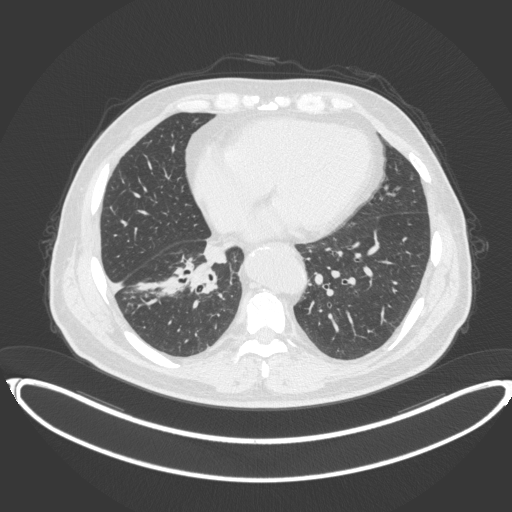
Chest CT, one axial slice. Position 151 of 383 along the scan axis. Reconstruction kernel B31f. Lung window (W 1500 / L -600 HU). 1 mm slice thickness. 512 × 512 image matrix, field of view 448 × 448 mm. Male patient, age 61 years. Case-level facts recorded for this patient, not image findings: clinical TNM (as recorded): T1b N1 M0.
Annotated regions visible in this slice (rectangle marked by the reading radiologist):
- lung tumour (recorded histology: squamous cell carcinoma): box from (x=163, y=256) to (x=217, y=298) px